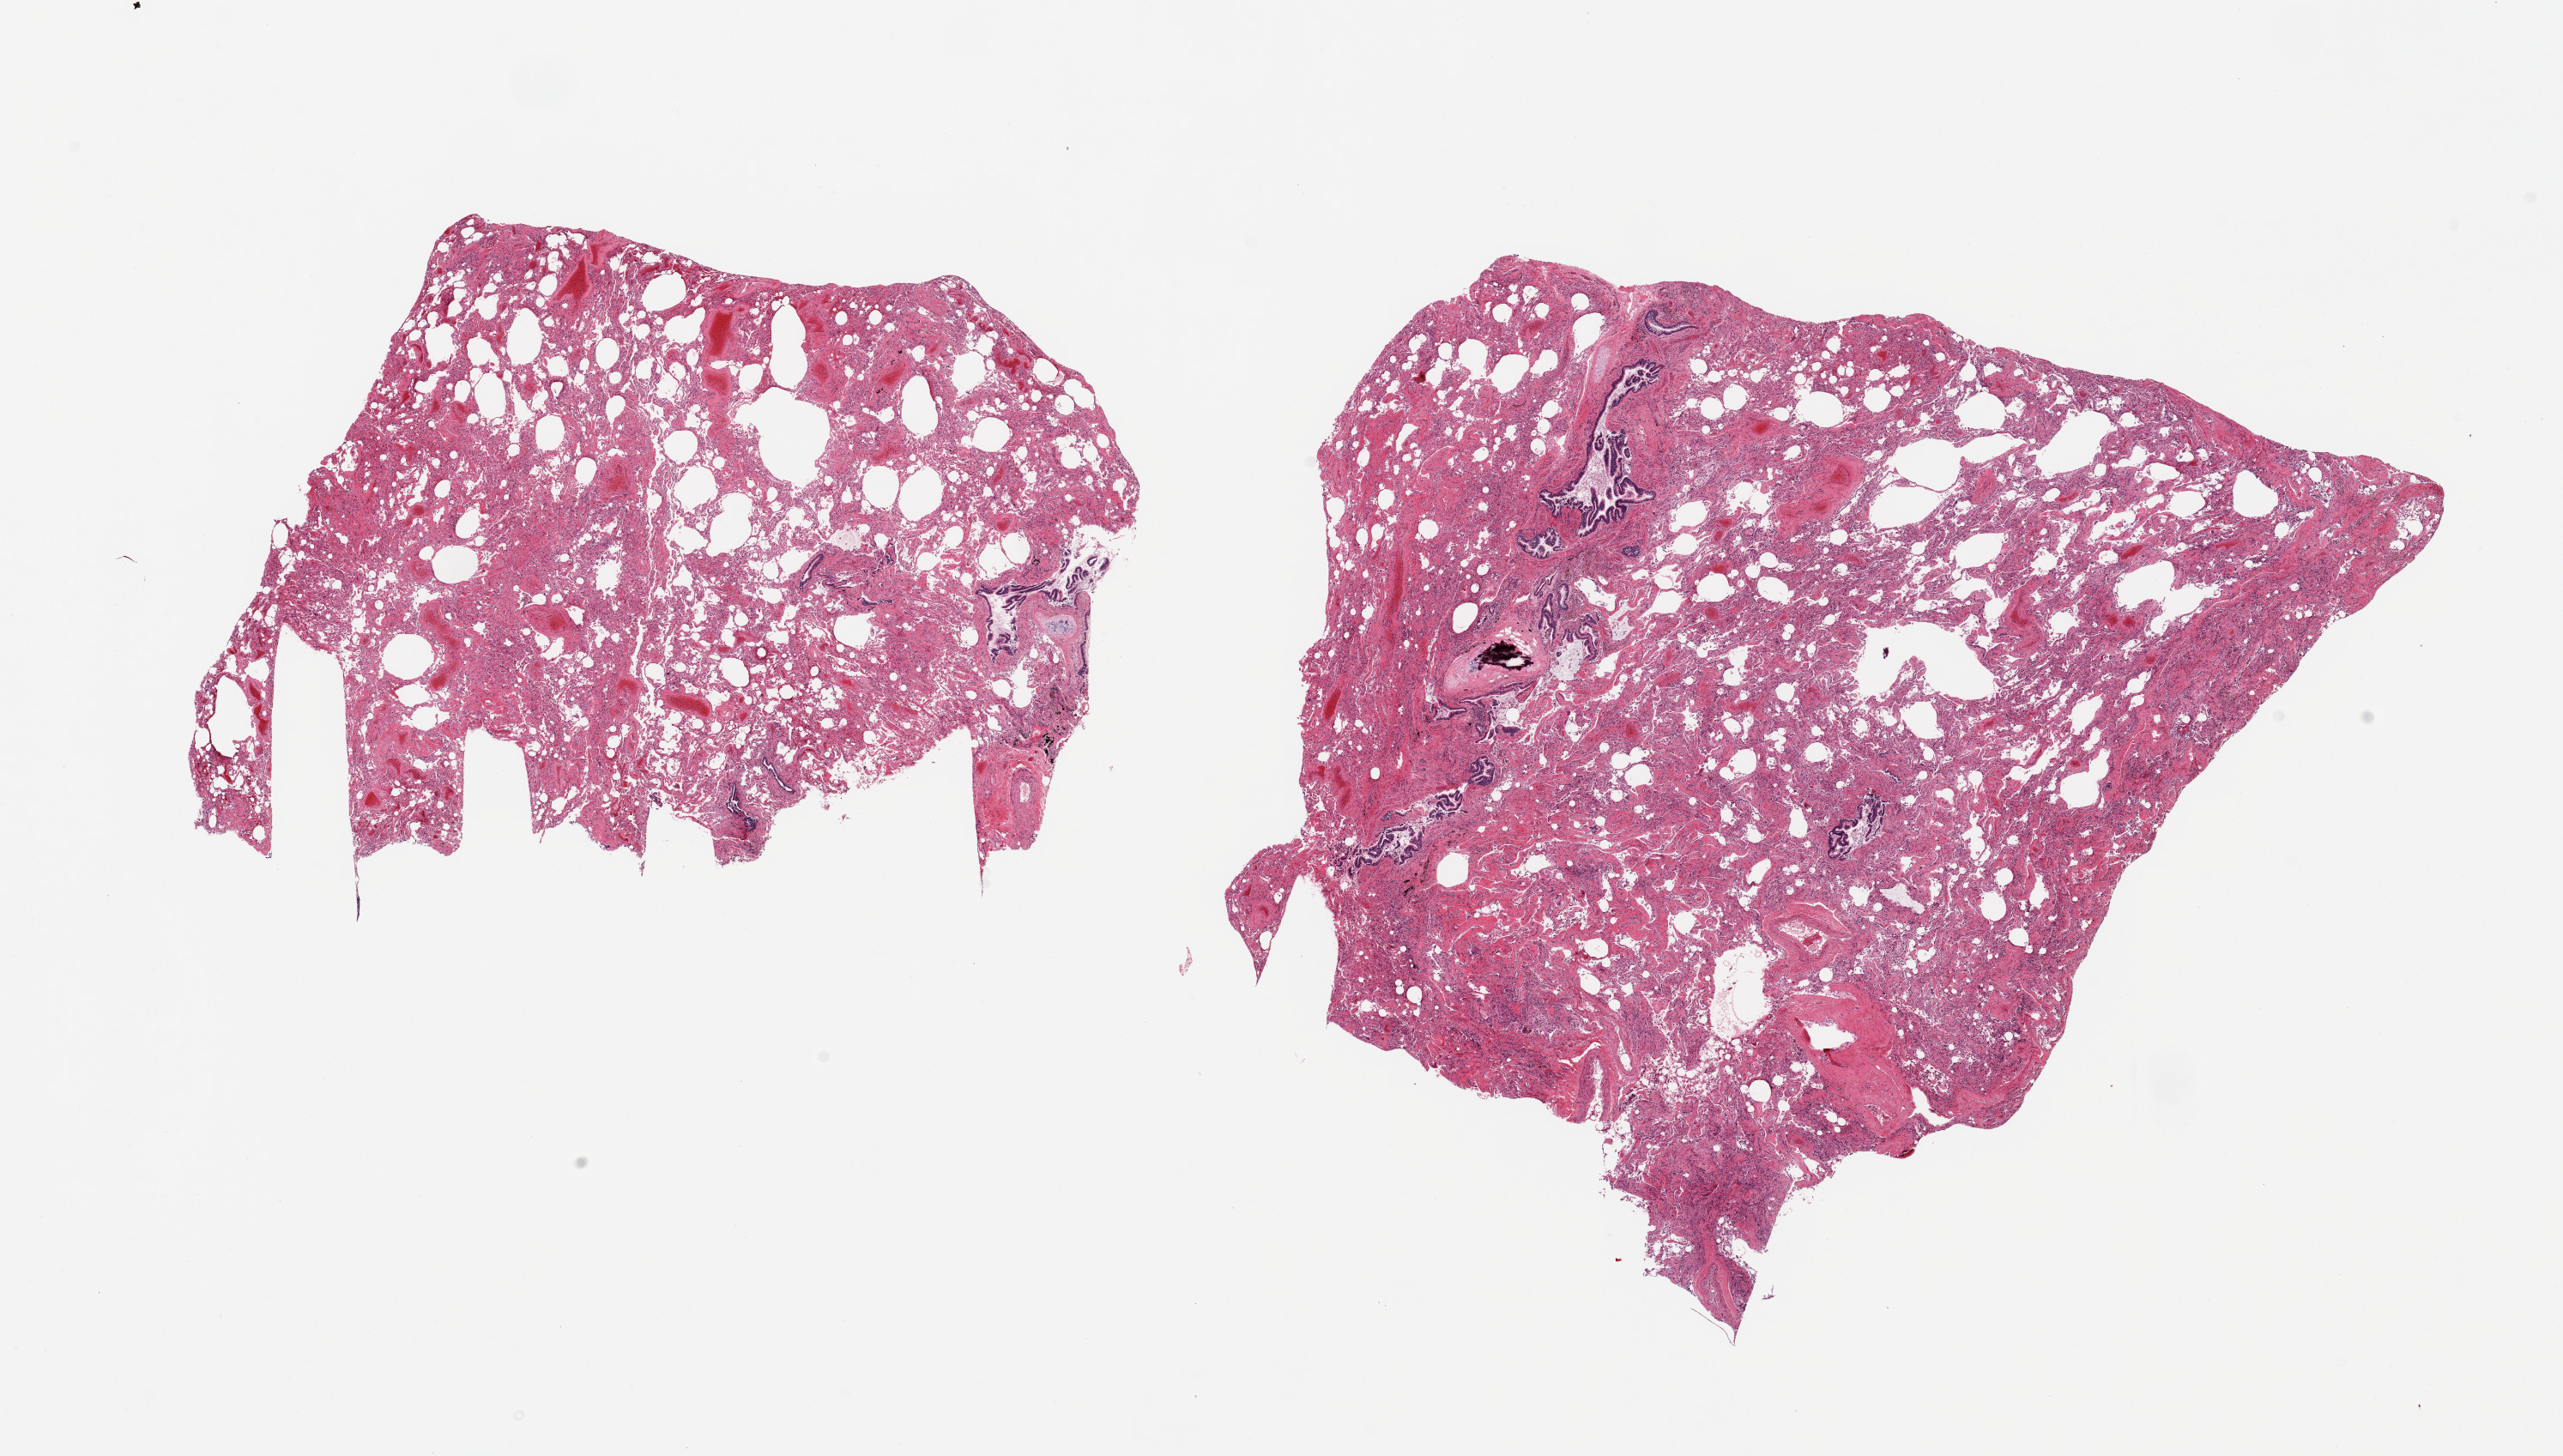
Digitized H&E-stained section, brightfield, a low-resolution overview of the entire scanned area, about 23.6 x 13.4 mm. PAXgene-fixed paraffin-embedded (PFPE) section. Section of lung (target tissue). Tissue donor sample.
Review note (as recorded): 2 pieces; emphysema, fibrosis, bronchiectasis; large bronchus with calcified cartilage sampled.